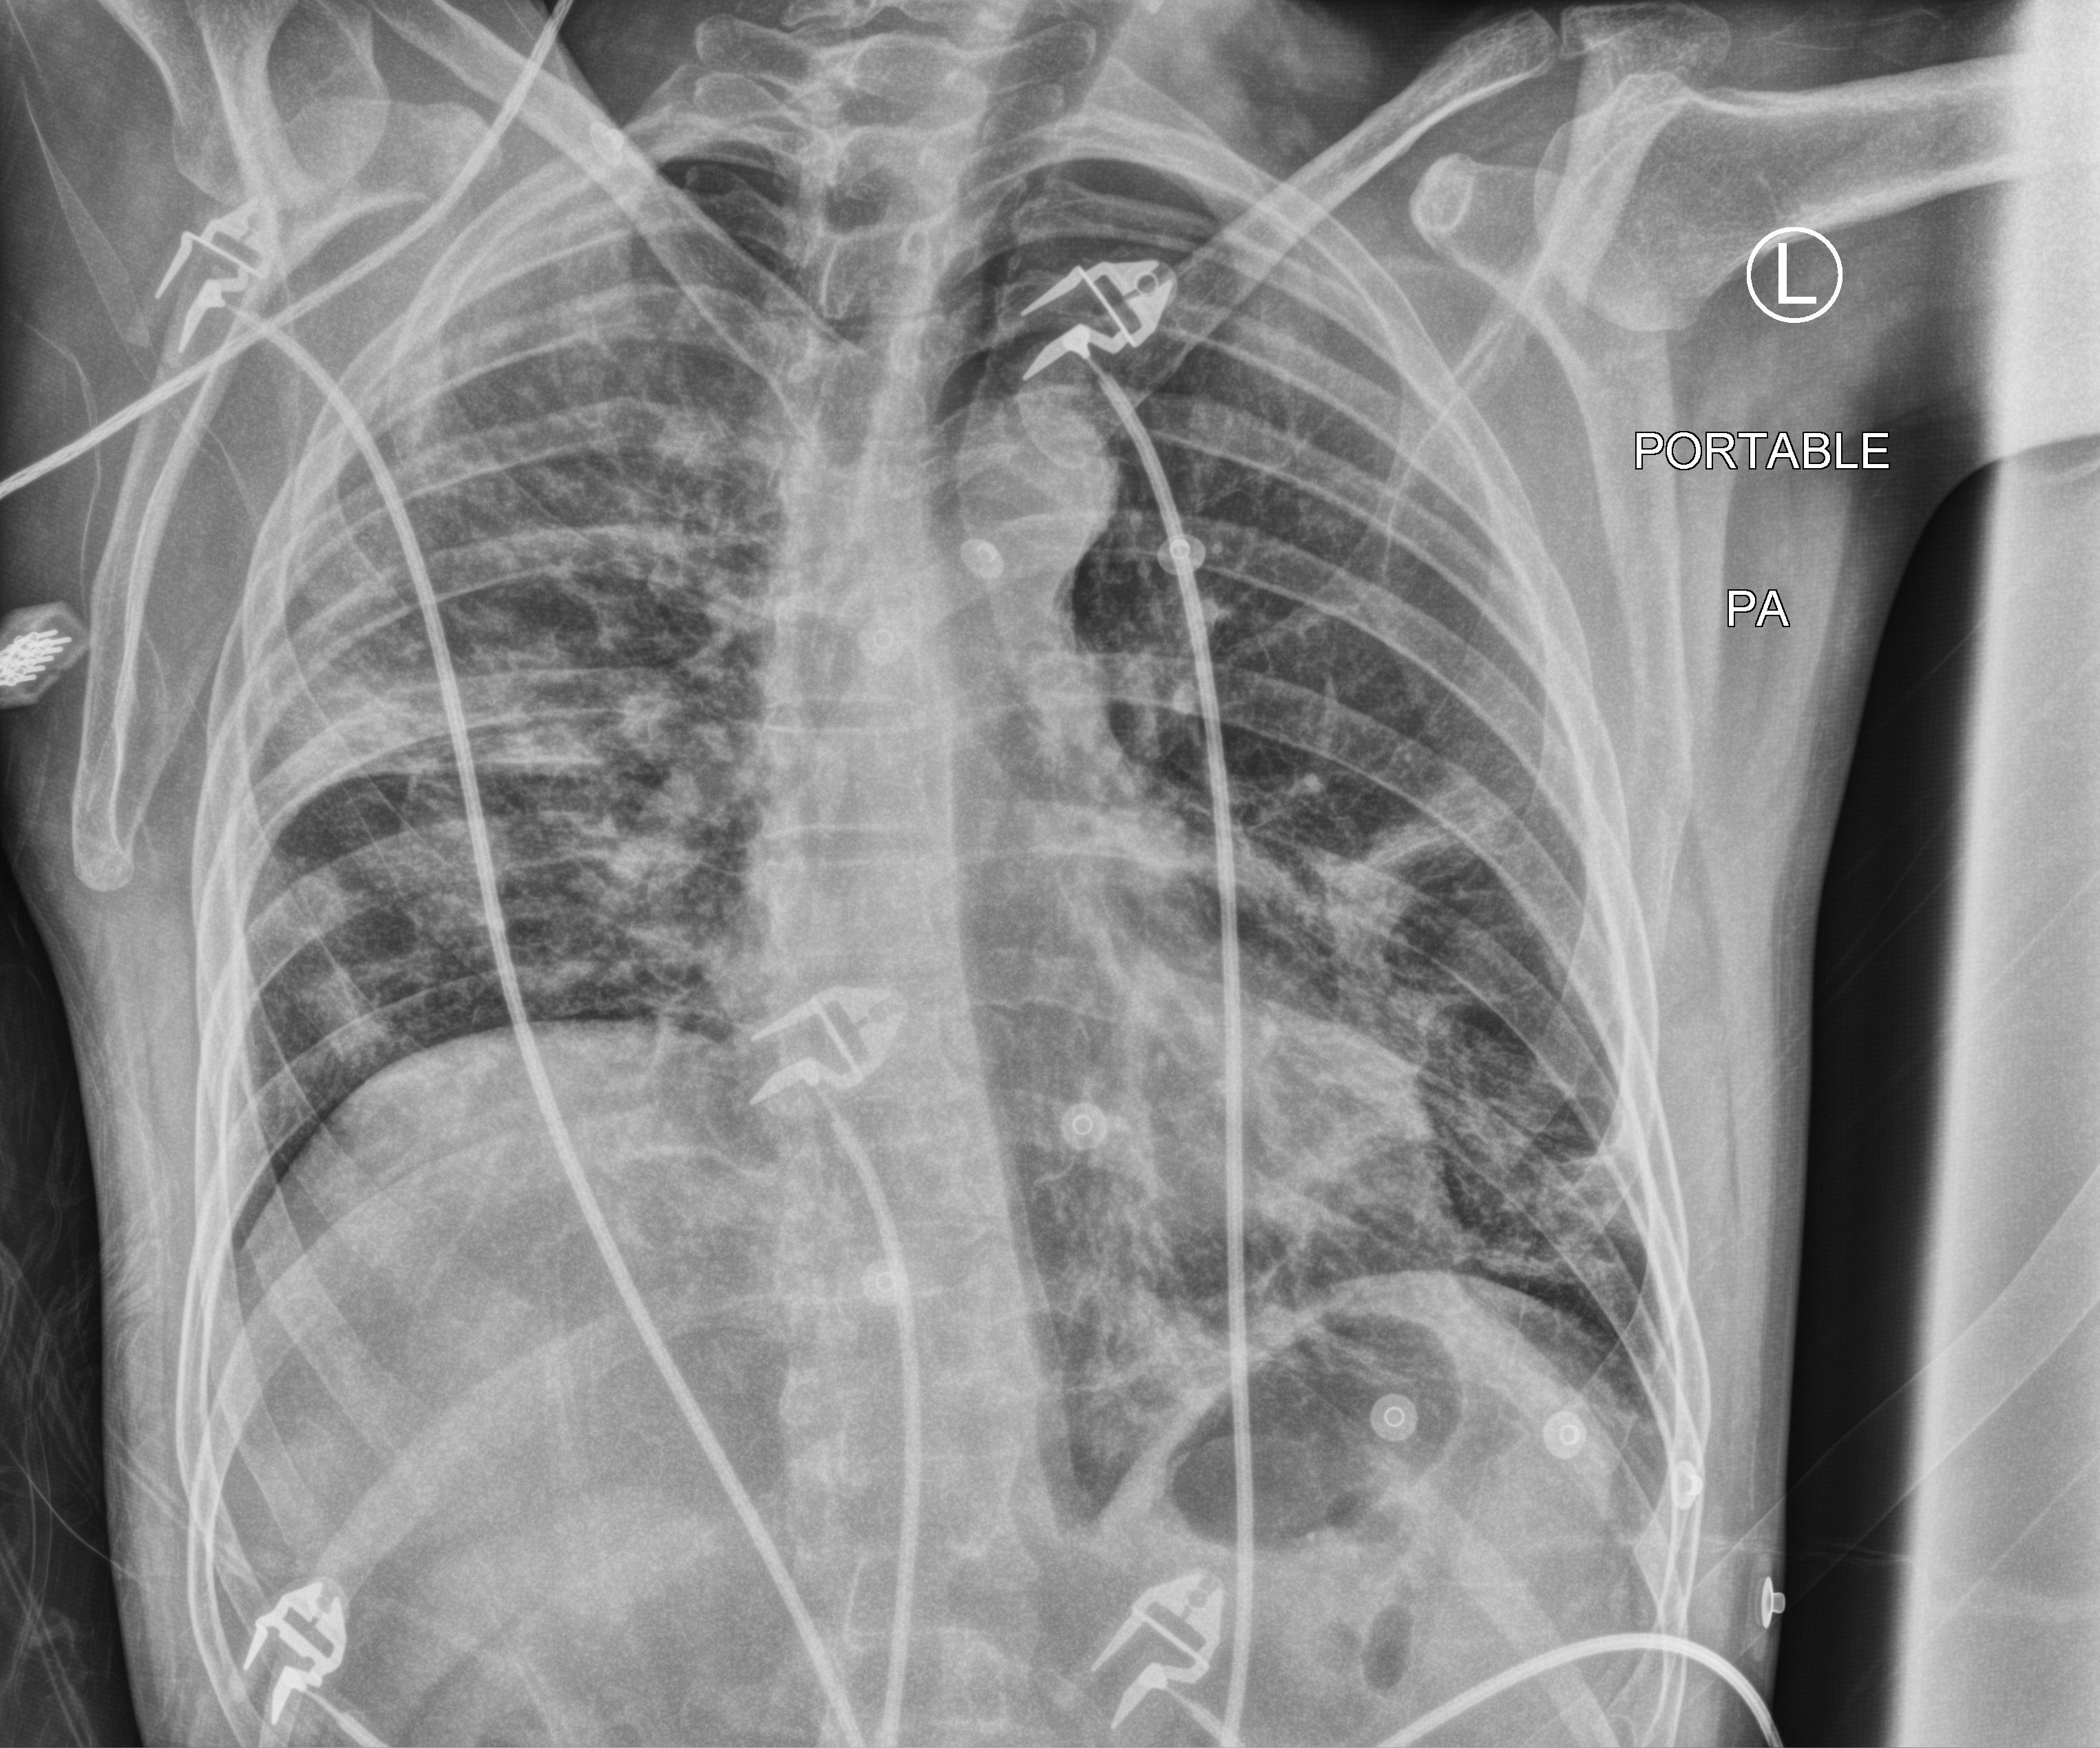
Chest X-ray; posteroanterior (PA) projection. Male patient hospitalised with COVID-19, age 18–59 years.
Hospital-stay facts (about this admission, not read from this image; timing relative to this image not recorded): admitted to intensive care during this hospital stay: no; mechanically ventilated during this hospital stay: no.